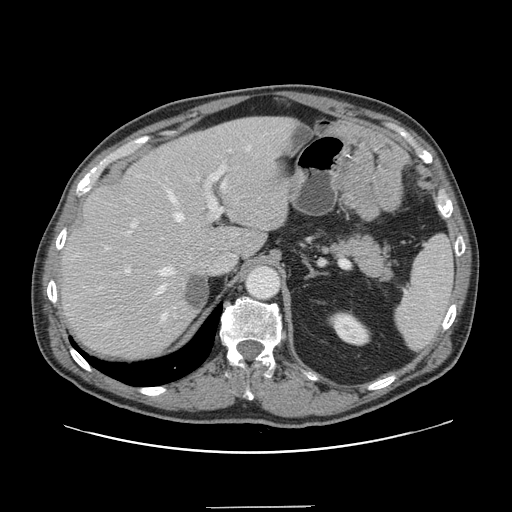
Contrast-enhanced abdominal CT, one axial slice; position 104 of 139 along the scan axis; intravenous contrast given; soft-tissue window (W 400 / L 40 HU); 2.5 mm slice thickness; 512 × 512 image matrix. Male patient, age 64 years. From the clinical record (not read from this slice): diagnosis: colorectal cancer liver metastases, imaged before liver resection; multiple liver metastases: yes; largest metastasis: 3.5 cm; disease in both lobes: yes.
Structures marked on this image (expert manual segmentation):
- hepatic veins: box from (x=106, y=146) to (x=250, y=321) px
- liver: (x=62, y=118)–(x=295, y=357)
- planned liver remnant (the part of the liver to remain after resection): (x=62, y=118)–(x=275, y=357)
- portal vein (with intrahepatic branches): (x=125, y=149)–(x=231, y=274)
- liver metastasis: (x=185, y=275)–(x=206, y=309)